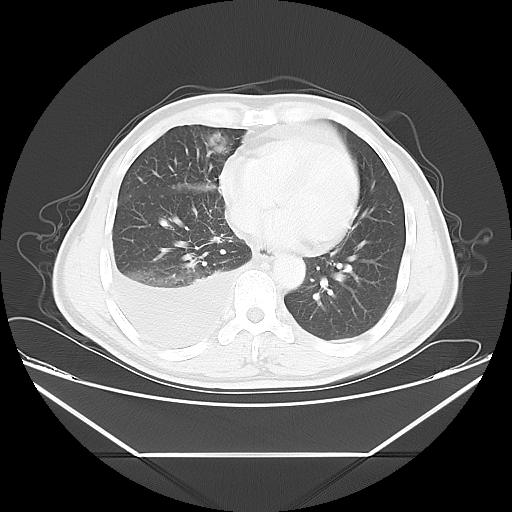
Chest CT, one axial slice; position 19 of 56 along the scan axis; reconstruction kernel LUNG; 120 kVp; lung window (W 1500 / L -600 HU); 5 mm slice thickness; 512 × 512 image matrix, field of view 412 × 412 mm. Patient: male, 57 years. From the clinical record (not read from this slice): clinical TNM (as recorded): T2 N3 M1.
Annotated regions visible in this slice (rectangle marked by the reading radiologist):
- lung tumour (recorded histology: adenocarcinoma): bounding box (x1, y1, x2, y2) in pixels: (204, 122, 231, 160)